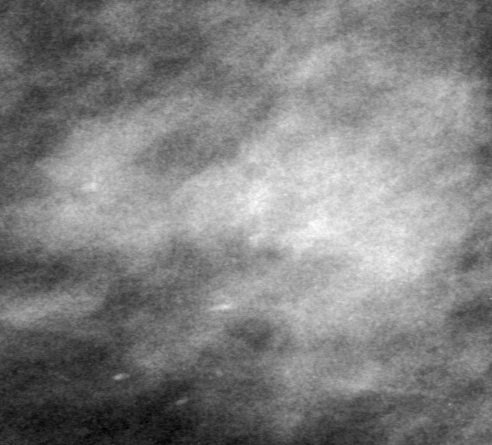
Crop from a digitized film mammogram around one marked abnormality, right breast, MLO view, BI-RADS breast density category 2 (scale 1–4).
Mass, shape lobulated, margins obscured; BI-RADS assessment category 0 (incomplete: needs additional imaging); pathology result (as recorded, not read from the image): benign.